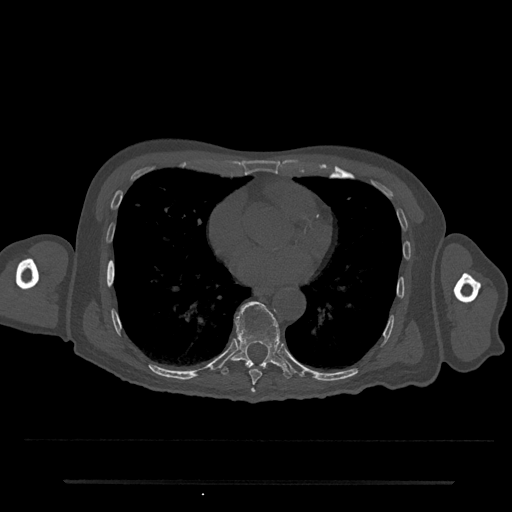
CT including the spine, one axial slice. Position 390 of 797 along the scan axis. Reconstruction kernel Br40s/3. 120 kVp. Bone window (W 1800 / L 400 HU). 512 × 512 image matrix, field of view 427 × 427 mm. Male patient, age 74 years. From the clinical record (not read from this slice): primary cancer: prostate.
Annotated regions visible in this slice (semi-automatic segmentation, software-assisted and operator-edited):
- T7 vertebra: bounding box [x1, y1, x2, y2] px = [251, 388, 256, 393]
- T8 vertebra: [249, 370, 262, 385]
- T9 vertebra: [221, 301, 292, 379]